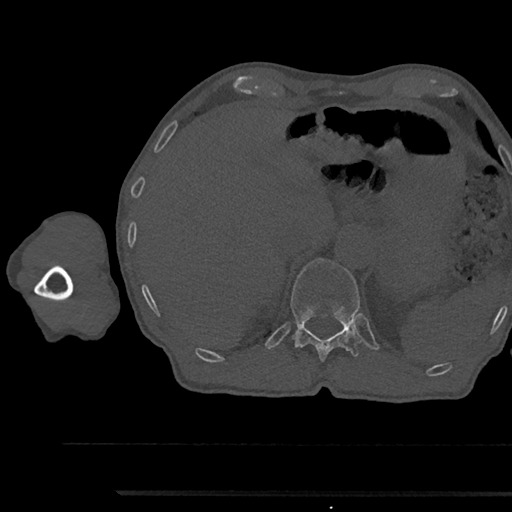
CT including the spine, one axial slice; position 715 of 797 along the scan axis; 120 kVp; bone window (W 1800 / L 400 HU); 512 × 512 image matrix, field of view 367 × 367 mm. Male patient, age 79 years. From the clinical record (not read from this slice): primary cancer: prostate.
Annotated regions visible in this slice (semi-automatic segmentation, software-assisted and operator-edited):
- T12 vertebra: bounding box [x1, y1, x2, y2] px = [290, 258, 363, 362]